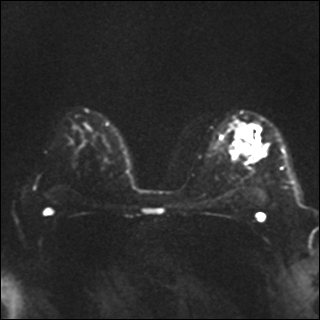
Breast MRI, one axial slice; slice 20 of 35 in the series (ordered by position); diffusion-weighted series; image 2 of 4 stored at this slice position (different b-values; order by instance number); 1.5 T; 4 mm slice thickness; 320 × 320 image matrix. Female patient.
Structures marked on this image (expert manual segmentation):
- tumour on diffusion-weighted imaging: bounding box (x1, y1, x2, y2) in pixels: (238, 145, 242, 150)